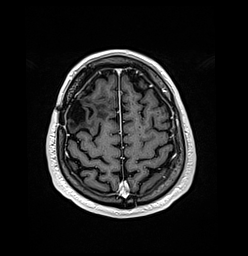
Brain MRI from a brain-tumour surgery series, one axial slice. Position 36 of 176 along the scan axis. T1-weighted post-contrast. 1 mm slice thickness. 248 × 256 image matrix, field of view 242 × 250 mm. From the clinical record (not read from this slice): histopathology: Oligodendroglioma; WHO grade: 3; IDH mutation: yes.
Structures marked on this image (manually delineated by an expert):
- previous resection cavity: bounding box [x1, y1, x2, y2] px = [69, 95, 86, 124]